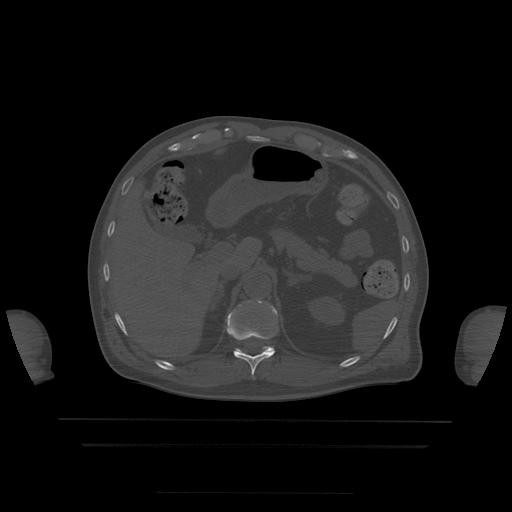
CT including the spine, one axial slice. Bone window (W 1800 / L 400 HU). 1.25 mm slice thickness. 512 × 512 image matrix. Patient age 68 years. From the clinical record (not read from this slice): primary cancer: urothelial.
Outlined on this slice (semi-automatically segmented with operator editing):
- T11 vertebra: bounding box (x1, y1, x2, y2) in pixels: (227, 312, 275, 376)
- T12 vertebra: (236, 305, 277, 353)